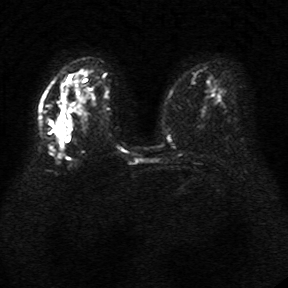
Breast MRI, one axial slice; slice 20 of 34 in the series (ordered by position); diffusion-weighted series; image 2 of 4 stored at this slice position (different b-values; order by instance number); 1.5 T; 5 mm slice thickness; 288 × 288 image matrix, field of view 340 × 340 mm. Female patient.
Outlined on this slice (manually delineated by an expert):
- tumour on diffusion-weighted imaging: box from (x=45, y=116) to (x=67, y=139) px